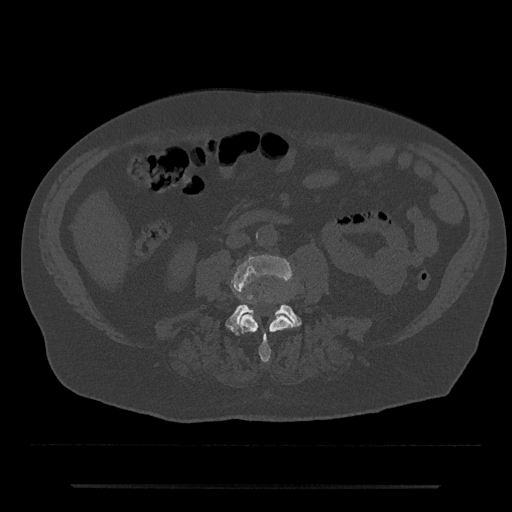
CT including the spine, one axial slice. Slice 381 of 797 in the series (ordered by position). Reconstruction kernel Br40s/3. Bone window (W 1800 / L 400 HU). 0.5 mm slice thickness. 512 × 512 image matrix. Patient: male, 80 years. From the clinical record (not read from this slice): primary cancer: prostate; vertebrae with lytic lesions (as recorded): L1, T11.
Annotated regions visible in this slice (semi-automatically segmented with operator editing):
- L3 vertebra: bounding box <232,255,293,362> (left, top, right, bottom; pixels)
- L4 vertebra: <225,296,302,335>